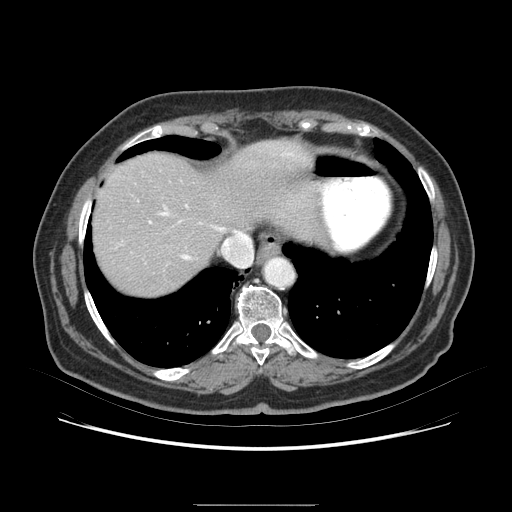
Contrast-enhanced abdominal CT (liver protocol), one axial slice. Slice 68 of 79 in the series (ordered by position). 120 kVp. Soft-tissue window (W 400 / L 40 HU). 2.5 mm slice thickness. 512 × 512 image matrix, field of view 380 × 380 mm. From the clinical record (not read from this slice): diagnosis: hepatocellular carcinoma (patient treated with transarterial chemoembolisation; whether this scan precedes or follows treatment is not stated here); TNM stage (as recorded): Stage-I; Child-Pugh class: A; tumour differentiation: poorly differentiated.
Structures marked on this image (semi-automatic segmentation, software-assisted and operator-edited):
- liver parenchyma outside the tumour (the mass and vessels are separate outlines, so this box may not span the whole liver): bounding box <98,160,218,274> (left, top, right, bottom; pixels)
- liver vessels: <155,231,164,238>